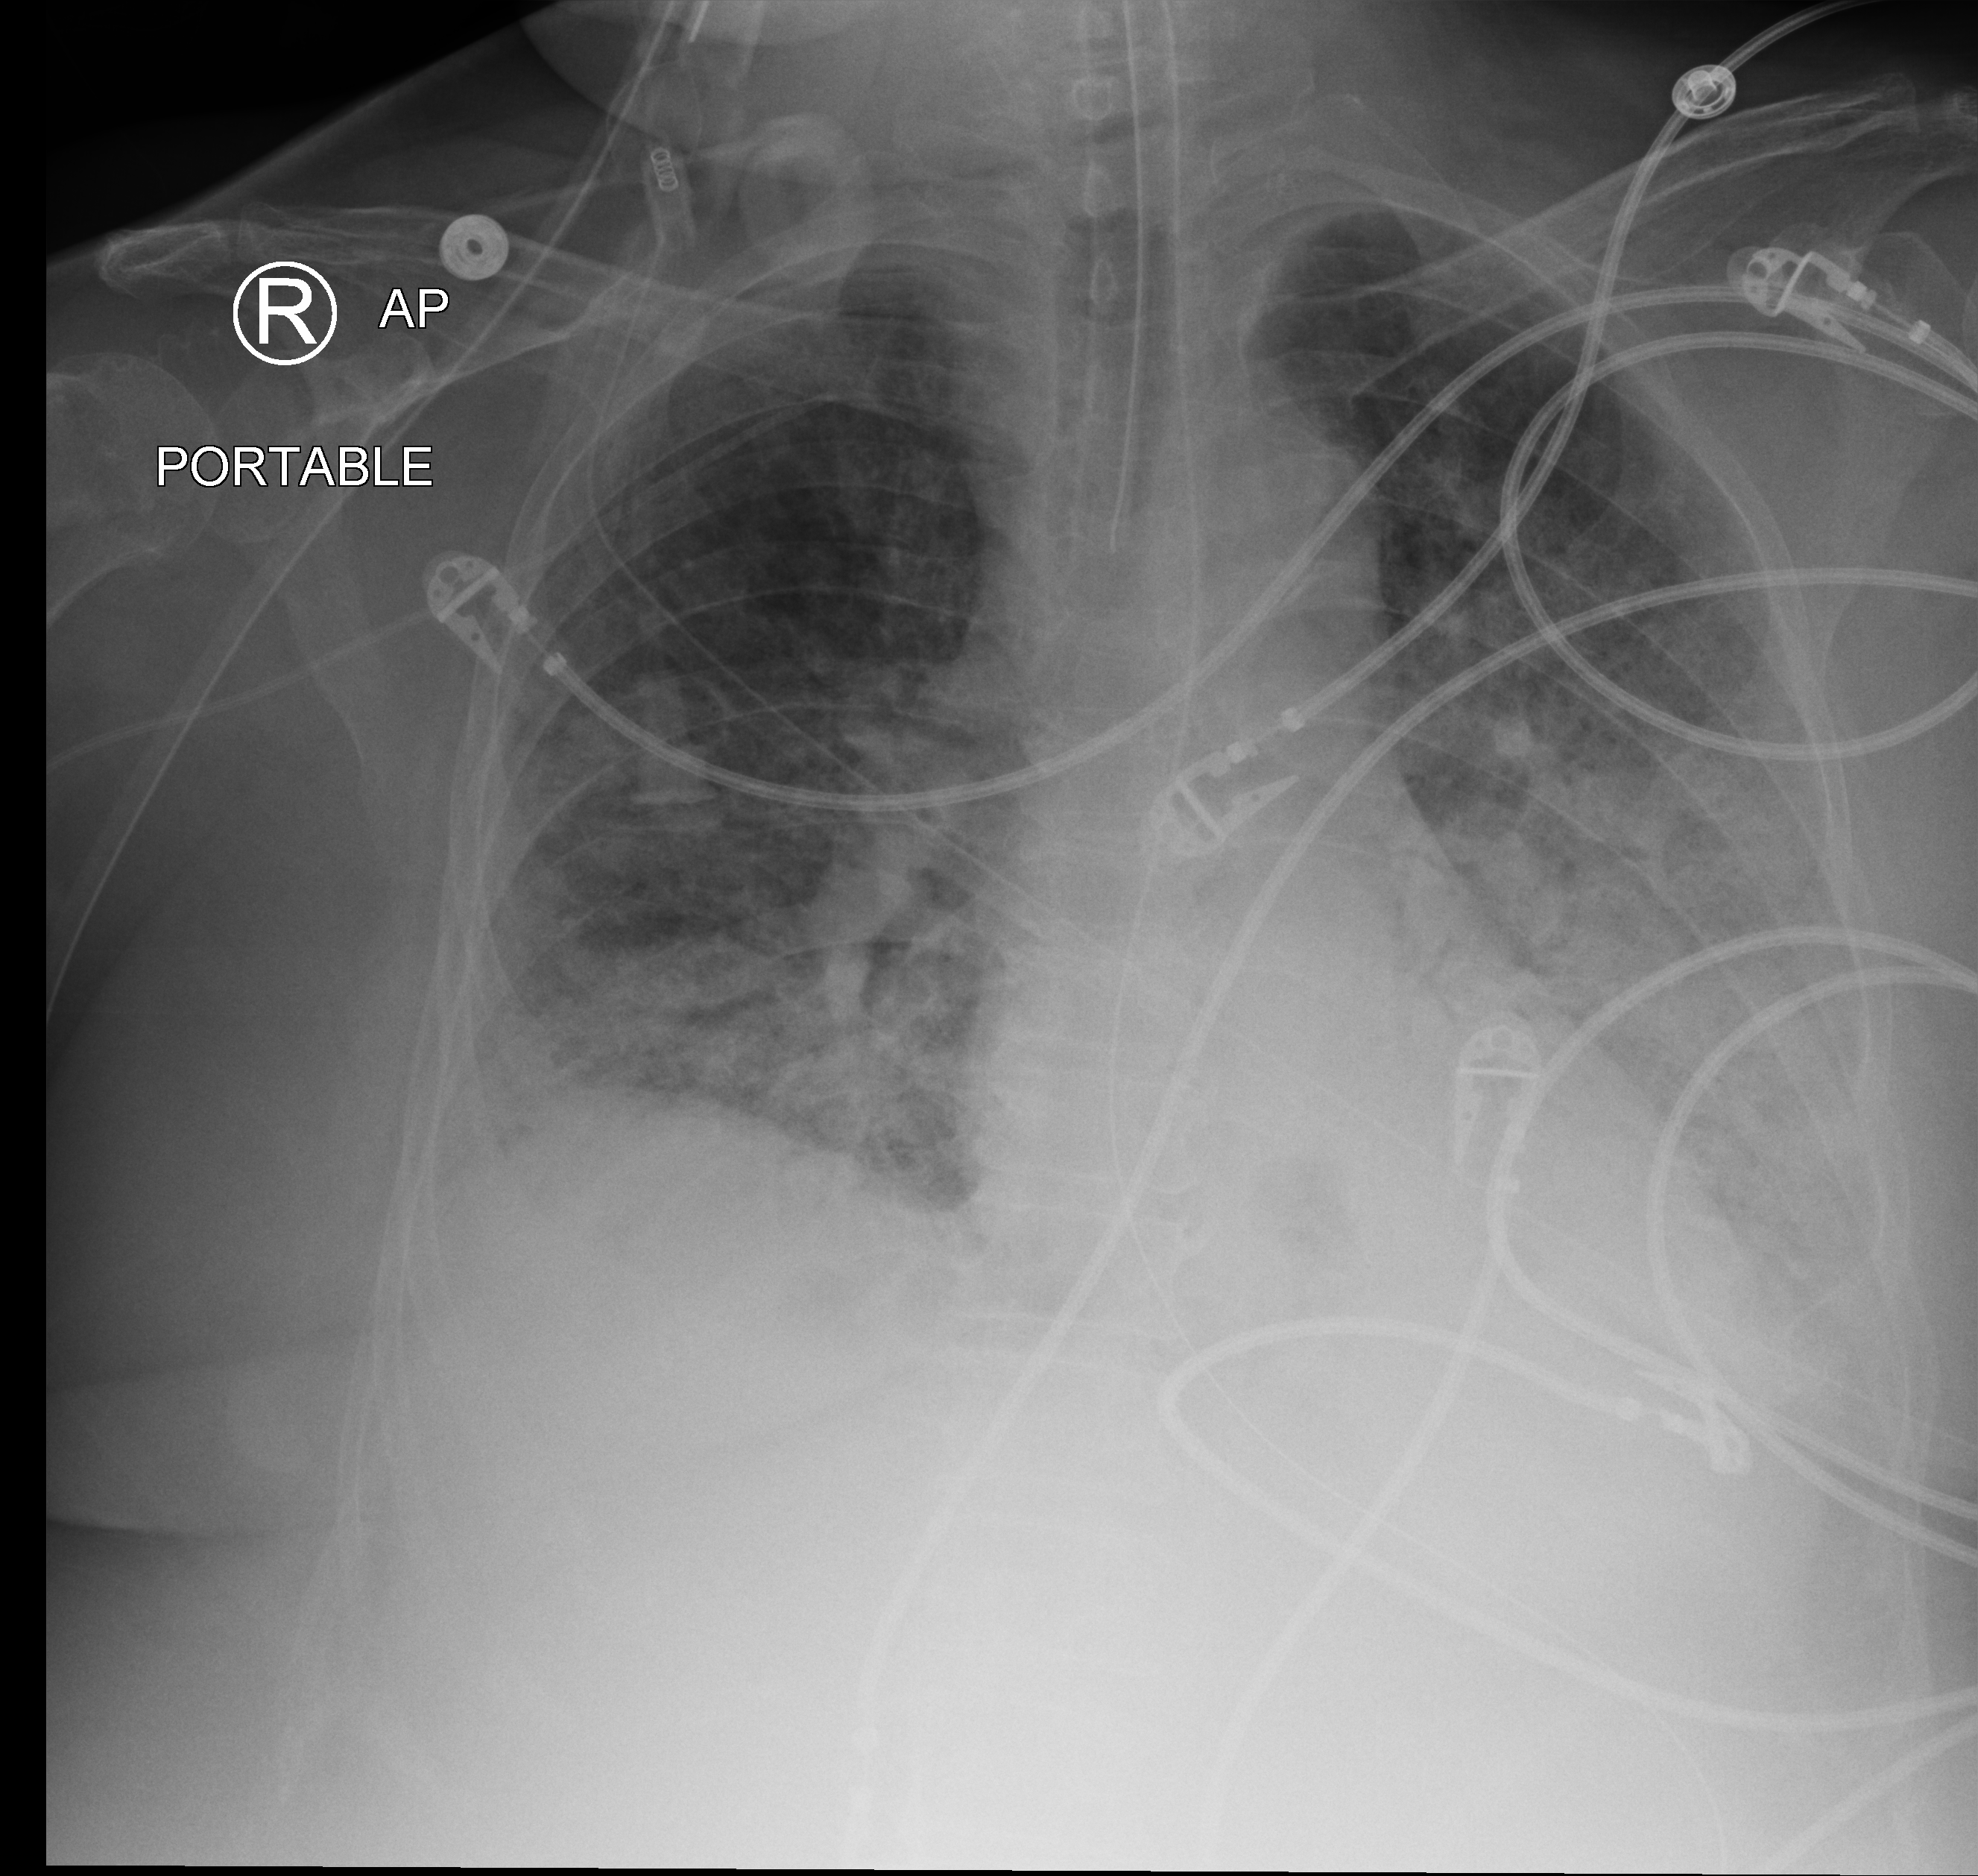
Chest X-ray (portable), anteroposterior (AP) projection. Patient hospitalised with COVID-19; female, aged 60–74 years.
Hospital-stay facts (about this admission, not read from this image; timing relative to this image not recorded): admitted to intensive care during this hospital stay: yes.